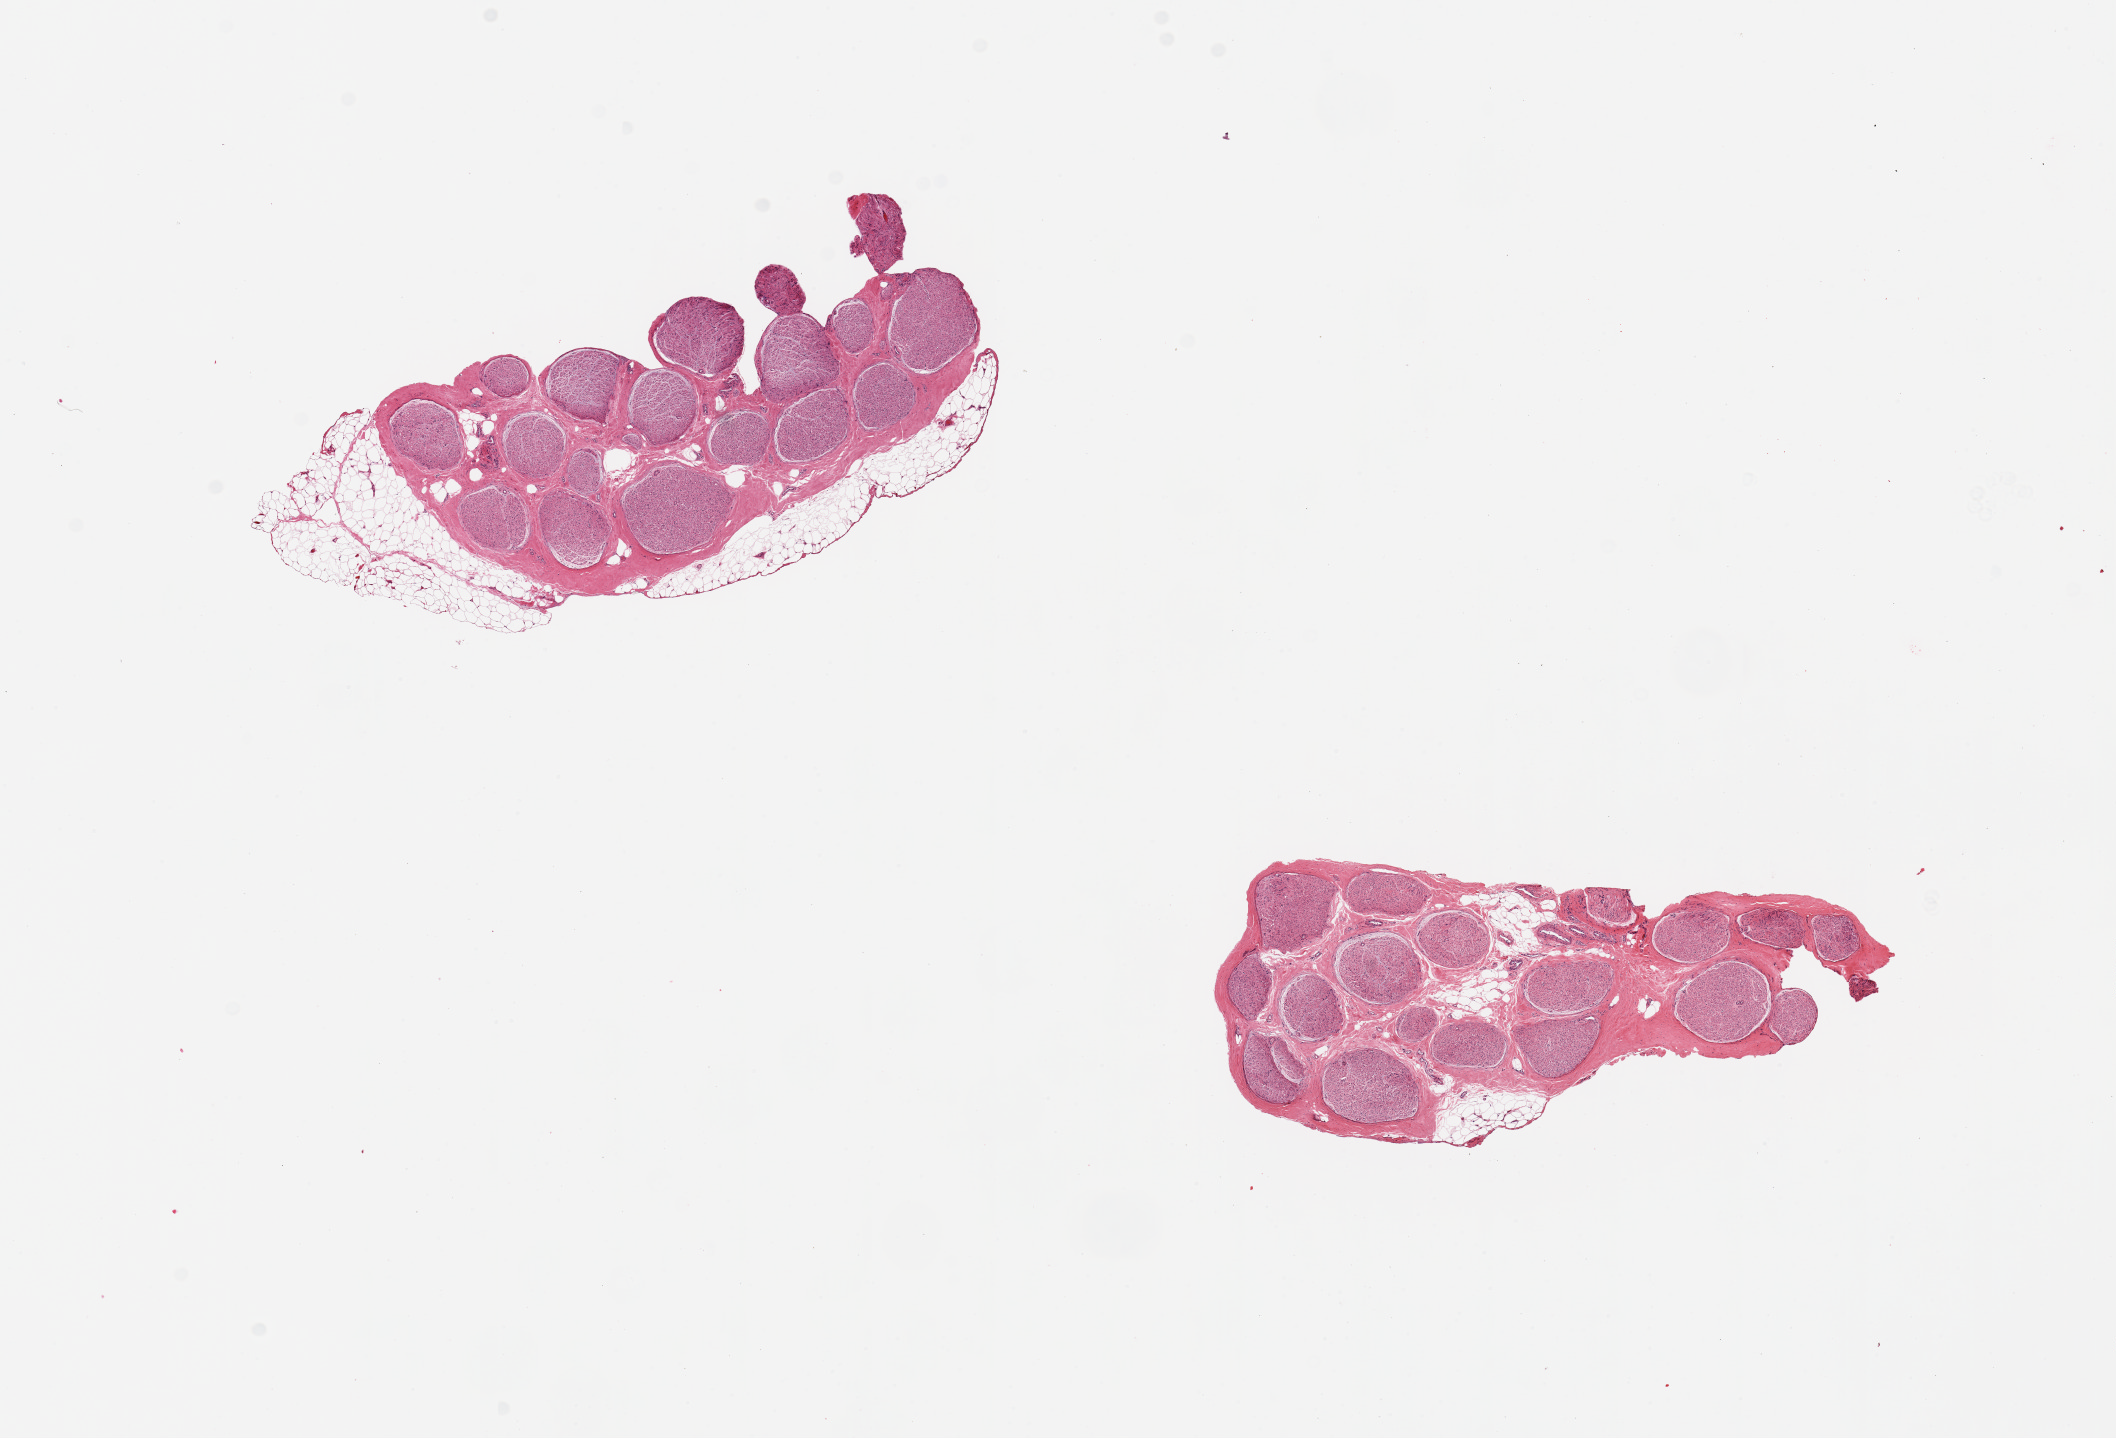
Whole-slide image, H&E stain, brightfield — low-resolution overview of the scanned area, about 16.7 x 11.4 mm; PAXgene-fixed, paraffin-embedded tissue; sampled site (target tissue): tibial nerve; tissue donor sample.
Review note (as recorded): 2 pieces; one piece has partial rim of attached fat up to 1.7mm (25%).